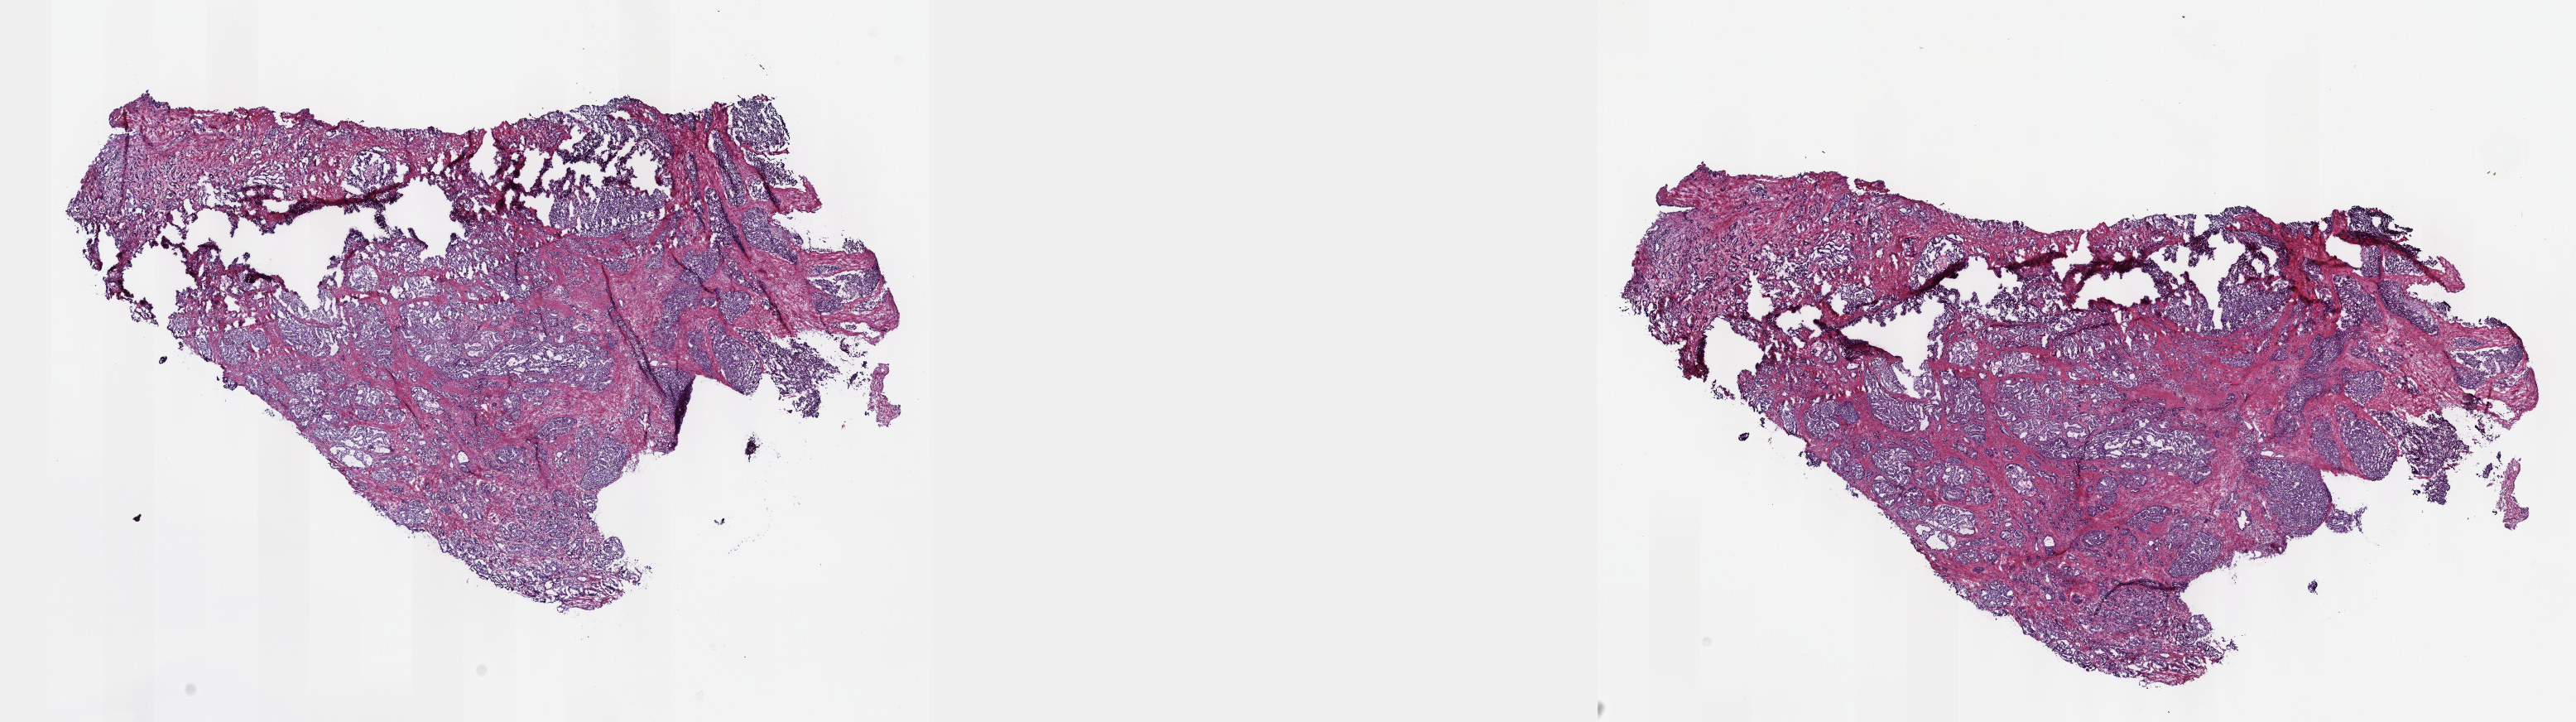
Digitized H&E tissue section (whole slide), whole scanned area (about 25.1 x 7.0 mm, slide scanned at 40x) shown as a low-resolution overview; frozen section from the top of the tissue portion; prostate, primary tumour sample. Male, age 66 years at initial diagnosis. Gleason score: 9 (4+5). Pathologist review of this section (percent, as recorded): tumour cells 60%, tumour nuclei 70%, normal cells 0%, stromal cells 40%, necrosis 0%. Infiltration values recorded for this section: lymphocyte infiltration 0%, monocyte infiltration 0%, neutrophil infiltration 0%.
Laterality: bilateral. Pathologic diagnosis: Adenocarcinoma, NOS (prostate gland). Lymph nodes positive (case pathology): 0 of 4 examined.